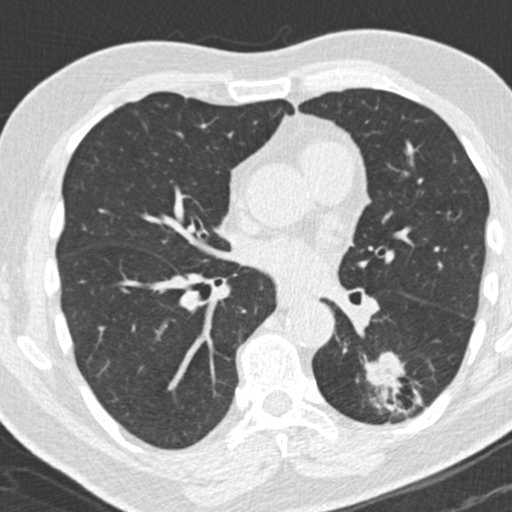
Axial slice from a low-dose chest CT screening exam; third annual screen; lung window (W 1500 / L -600 HU); slice 83 of 180 in the series. Male, age 66 years at enrolment. Former smoker at enrolment.
• Expert-annotated lung lesion, bounding box [x1, y1, x2, y2] px = [356, 353, 425, 427].
• Reader record for this screening exam (exam-level; its link to the box is not recorded): non-calcified nodule or mass ≥4 mm, left lower lobe, 31 × 24 mm, spiculated (stellate) margins, pre-existing on the prior screen: yes; interval growth: yes.
• Lung cancer was diagnosed 56 days after this screen: adenocarcinoma, NOS, left lower lobe, poorly differentiated (G3), stage IB (AJCC 6th edition), 38 mm at pathology.